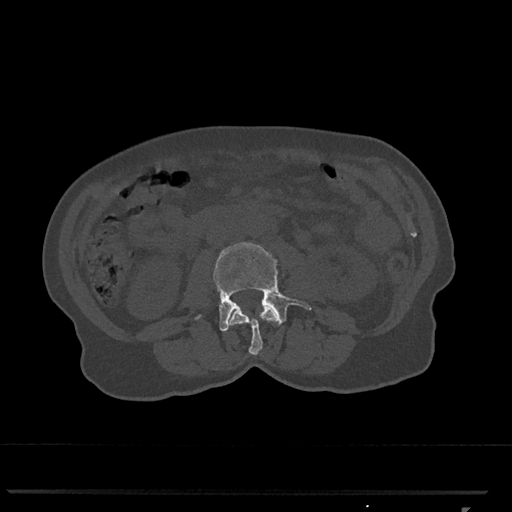
CT including the spine, one axial slice; slice 295 of 793 in the series (ordered by position); bone window (W 1800 / L 400 HU); 0.5 mm slice thickness; 512 × 512 image matrix, field of view 380 × 380 mm. Female patient, age 62 years. From the clinical record (not read from this slice): primary cancer: renal.
Structures marked on this image (semi-automatic segmentation, software-assisted and operator-edited):
- L2 vertebra: bounding box [x1, y1, x2, y2] px = [228, 306, 278, 355]
- L3 vertebra: [195, 242, 312, 332]